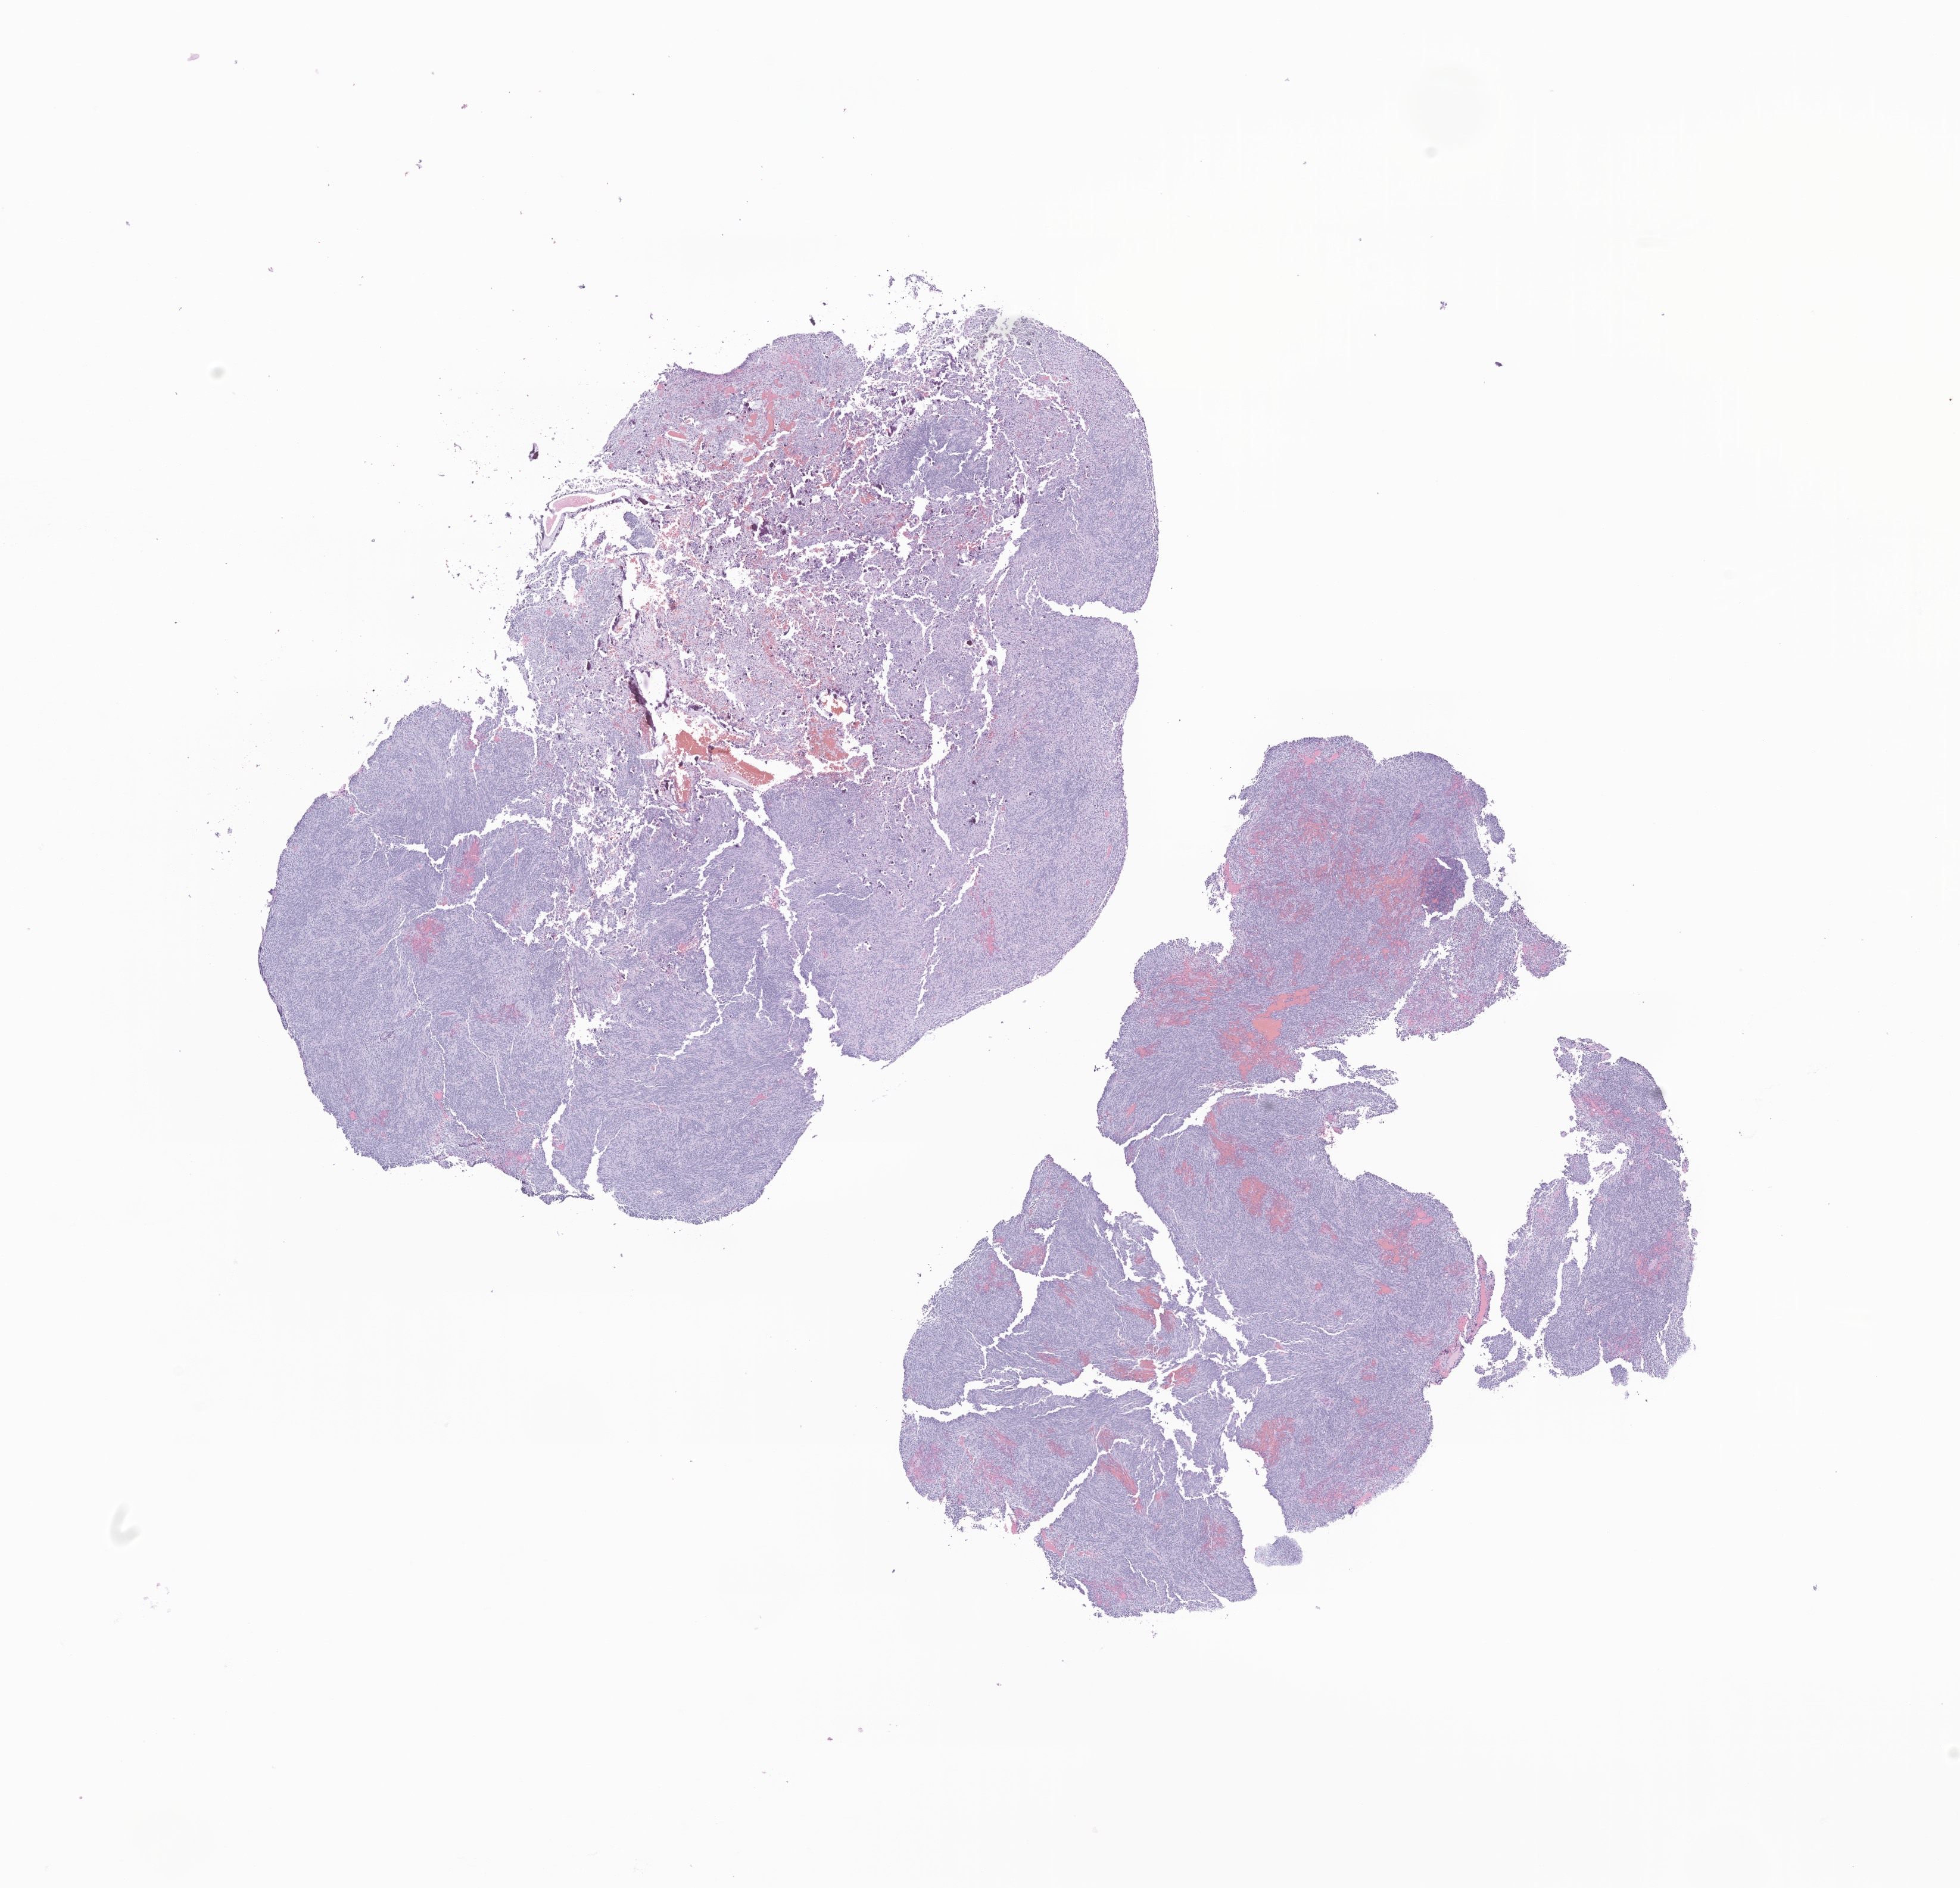
H&E whole-slide image of tumor tissue from the brain — whole scanned area (about 13.9 x 13.4 mm) shown as a low-resolution overview; FFPE section. Female patient, age 58 months (4 years 10 months).
Recorded diagnosis: Atypical teratoid/rhabdoid tumor.